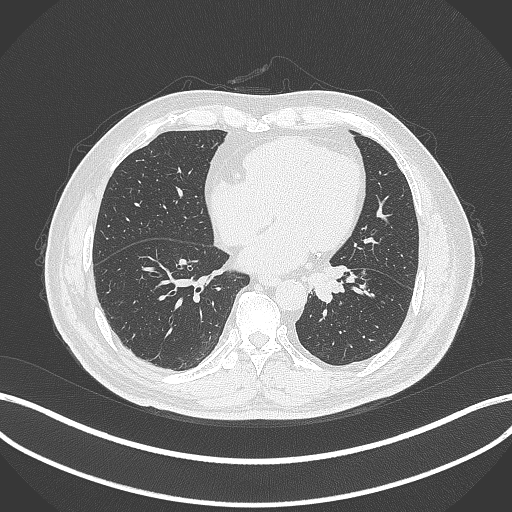
Chest CT, one axial slice. Slice 98 of 312 in the series (ordered by position). Reconstruction kernel B70f. 120 kVp. Lung window (W 1500 / L -600 HU). 1 mm slice thickness. 512 × 512 image matrix, field of view 400 × 400 mm. Patient: male, 71 years. From the clinical record (not read from this slice): clinical TNM (as recorded): T1b N0 M0.
Outlined on this slice (rectangle marked by the reading radiologist):
- lung tumour (recorded histology: squamous cell carcinoma): bounding box (x1, y1, x2, y2) in pixels: (308, 264, 356, 304)